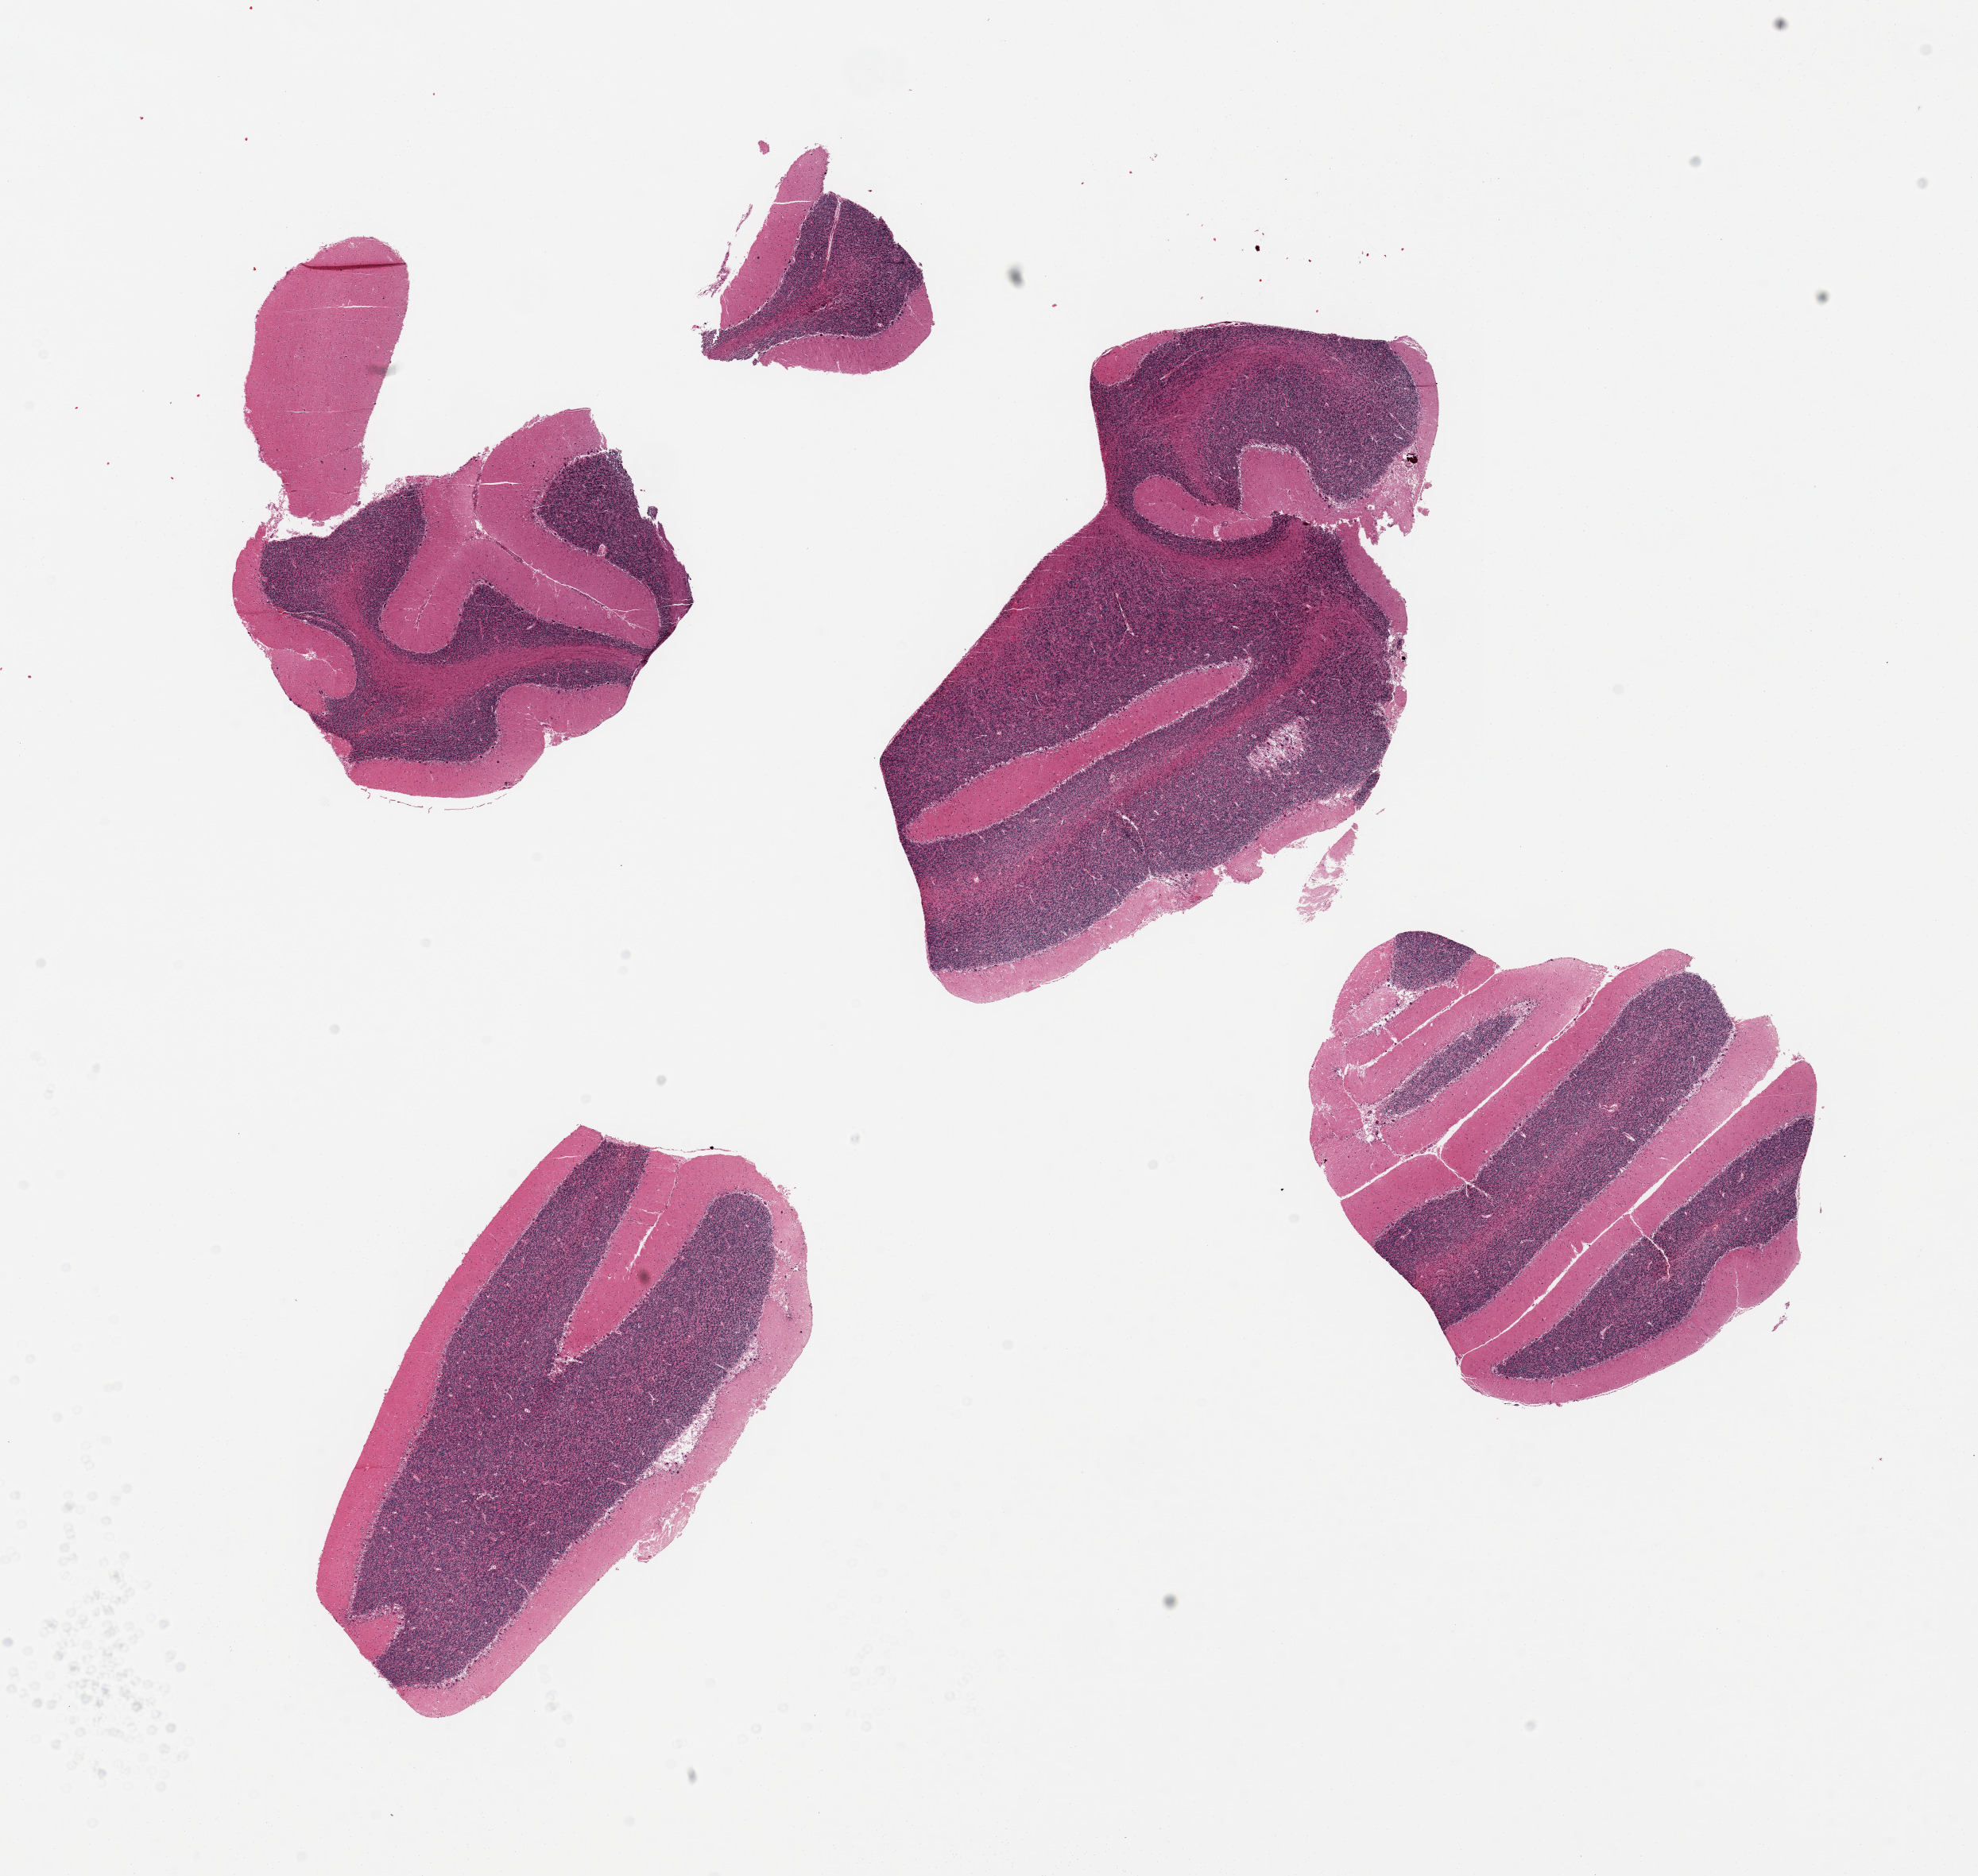
Haematoxylin and eosin whole-slide image, low-resolution overview of the scanned area, about 19.7 x 18.7 mm (slide scanned at 20x), PAXgene-fixed, paraffin-embedded tissue, target tissue: cerebellum, tissue donor sample. Donor: male.
* pathologist's review note for this sample: 4 pieces (fragmented)--no abnormalities; Purkinje cells well visualized